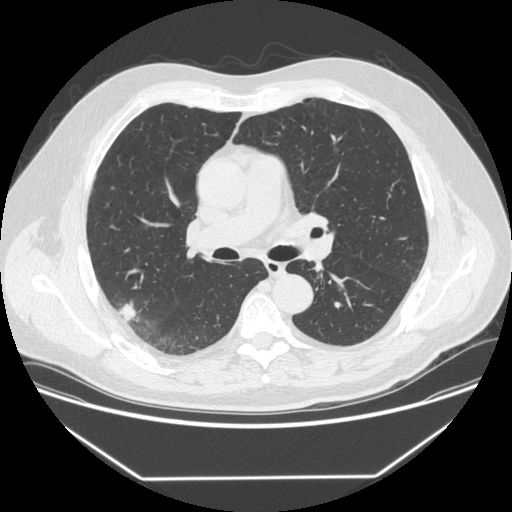
Axial slice from a low-dose chest CT screening exam. Baseline annual screen. Lung window (W 1500 / L -600 HU). 1.25 mm slice thickness. Slice 214 of 342 in the series. 512 × 512 image matrix, field of view 410 × 410 mm. Male participant, aged 64 years at enrolment. Former smoker at enrolment.
Expert-annotated lung lesion, bounding box <102,299,144,333> (left, top, right, bottom; pixels). The exam's reader record, not a measurement of the box and not confirmed to be the same lesion: non-calcified nodule or mass ≥4 mm, right upper lobe, 12 × 12 mm, smooth margins, soft tissue attenuation. Official screen result: positive, change unspecified: nodule(s) >= 4 mm or enlarging nodule(s), mass(es), or other non-specific abnormalities suspicious for lung cancer. Lung cancer was diagnosed 92 days after this screen: adenocarcinoma, NOS, right upper lobe, poorly differentiated (G3), stage IIIB (AJCC 6th edition), 15 mm at pathology.